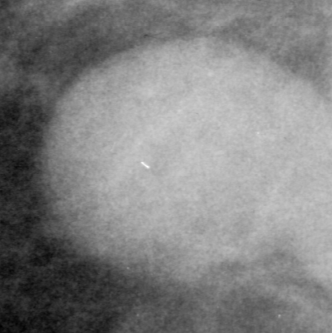
Region of interest cut from a scanned film mammogram (one marked finding); left breast; MLO view; BI-RADS breast density category 4 (scale 1–4).
Mass, shape lobulated, margins circumscribed; BI-RADS assessment category 4; subtlety rating 4 on a 1 (subtle) to 5 (obvious) scale; pathology (as recorded): benign.